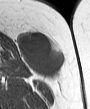
MRI of an extremity soft-tissue mass, one axial slice; slice 20 of 45 in the series (ordered by position); MR volume resampled by the dataset authors to the PET/CT grid (not the native acquisition matrix); 3.27 mm slice thickness; 90 × 109 image matrix, field of view 88 × 106 mm. Female patient. From the clinical record (not read from this slice): histological type: leiomyosarcoma; grade: intermediate; site of the primary tumour: parascapusular.
Structures marked on this image (expert contour drawn on MRI and transferred to this co-registered scan by the dataset authors):
- gross tumour volume including surrounding oedema: bounding box <17,32,63,79> (left, top, right, bottom; pixels)
- gross tumour volume (mass): <17,32,63,79>